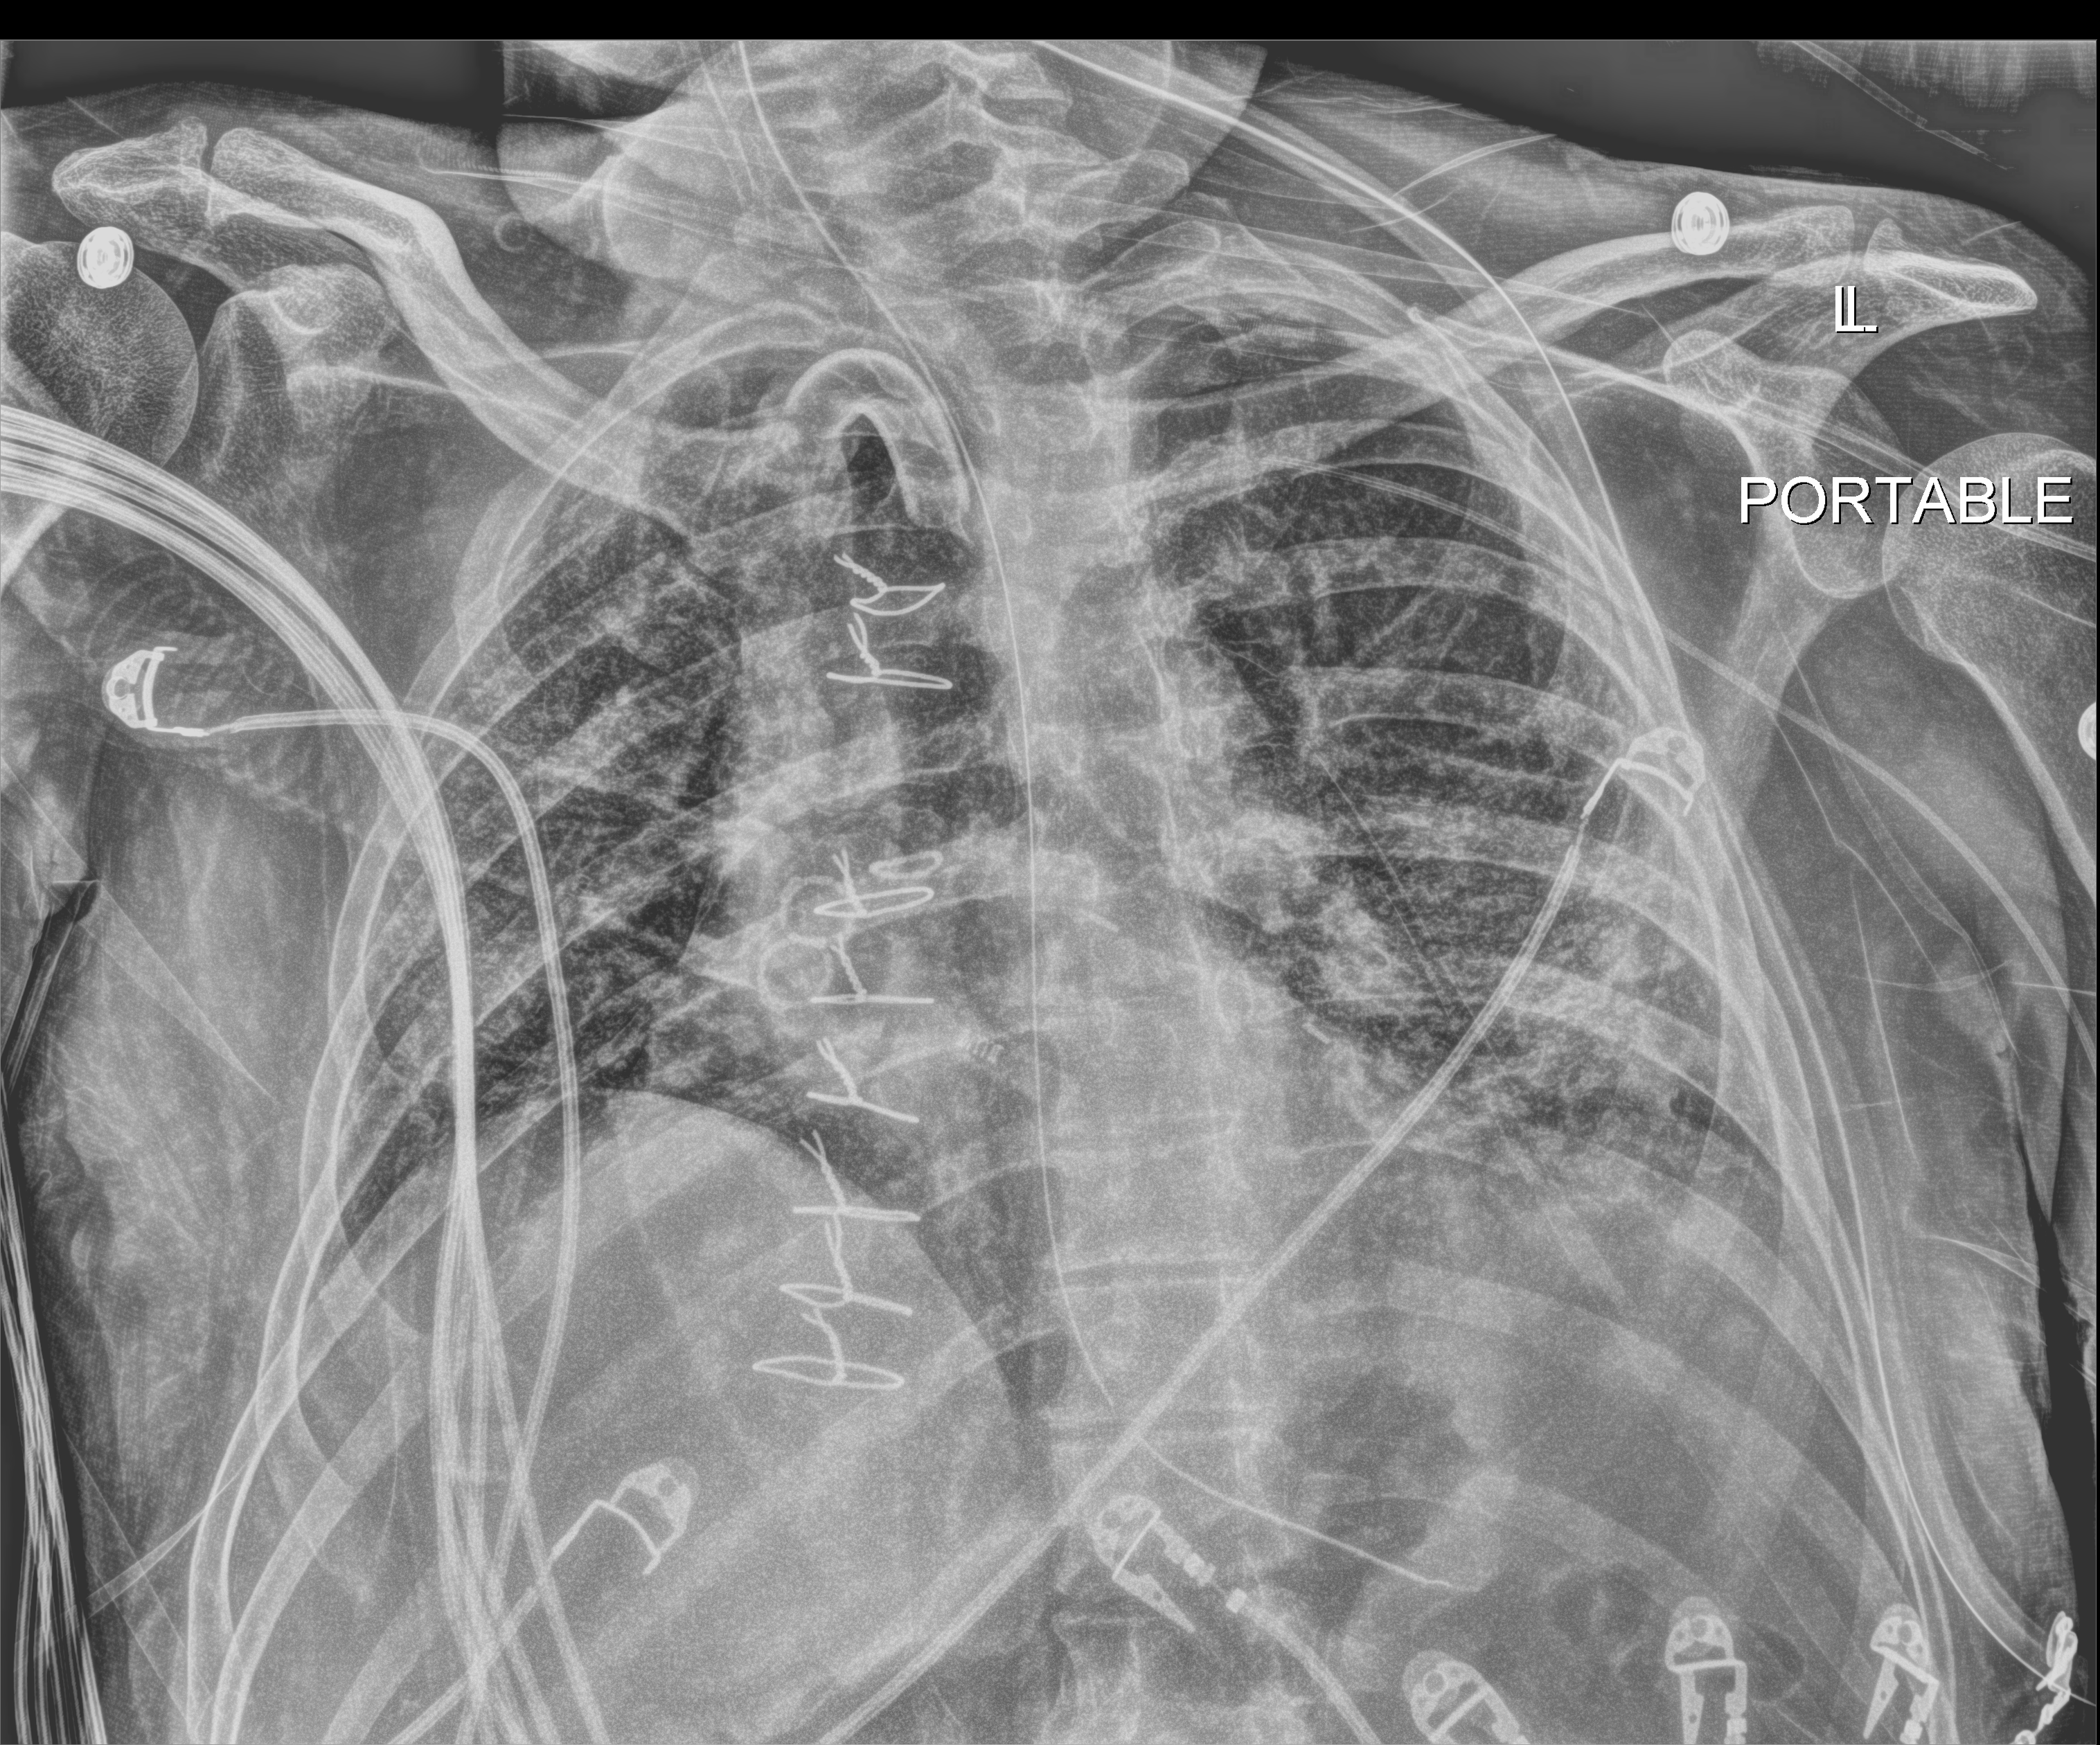
Chest X-ray (portable). Male patient hospitalised with COVID-19, age 18–59 years.
Hospital-stay facts (about this admission, not read from this image; timing relative to this image not recorded):
- admitted to intensive care during this hospital stay: yes